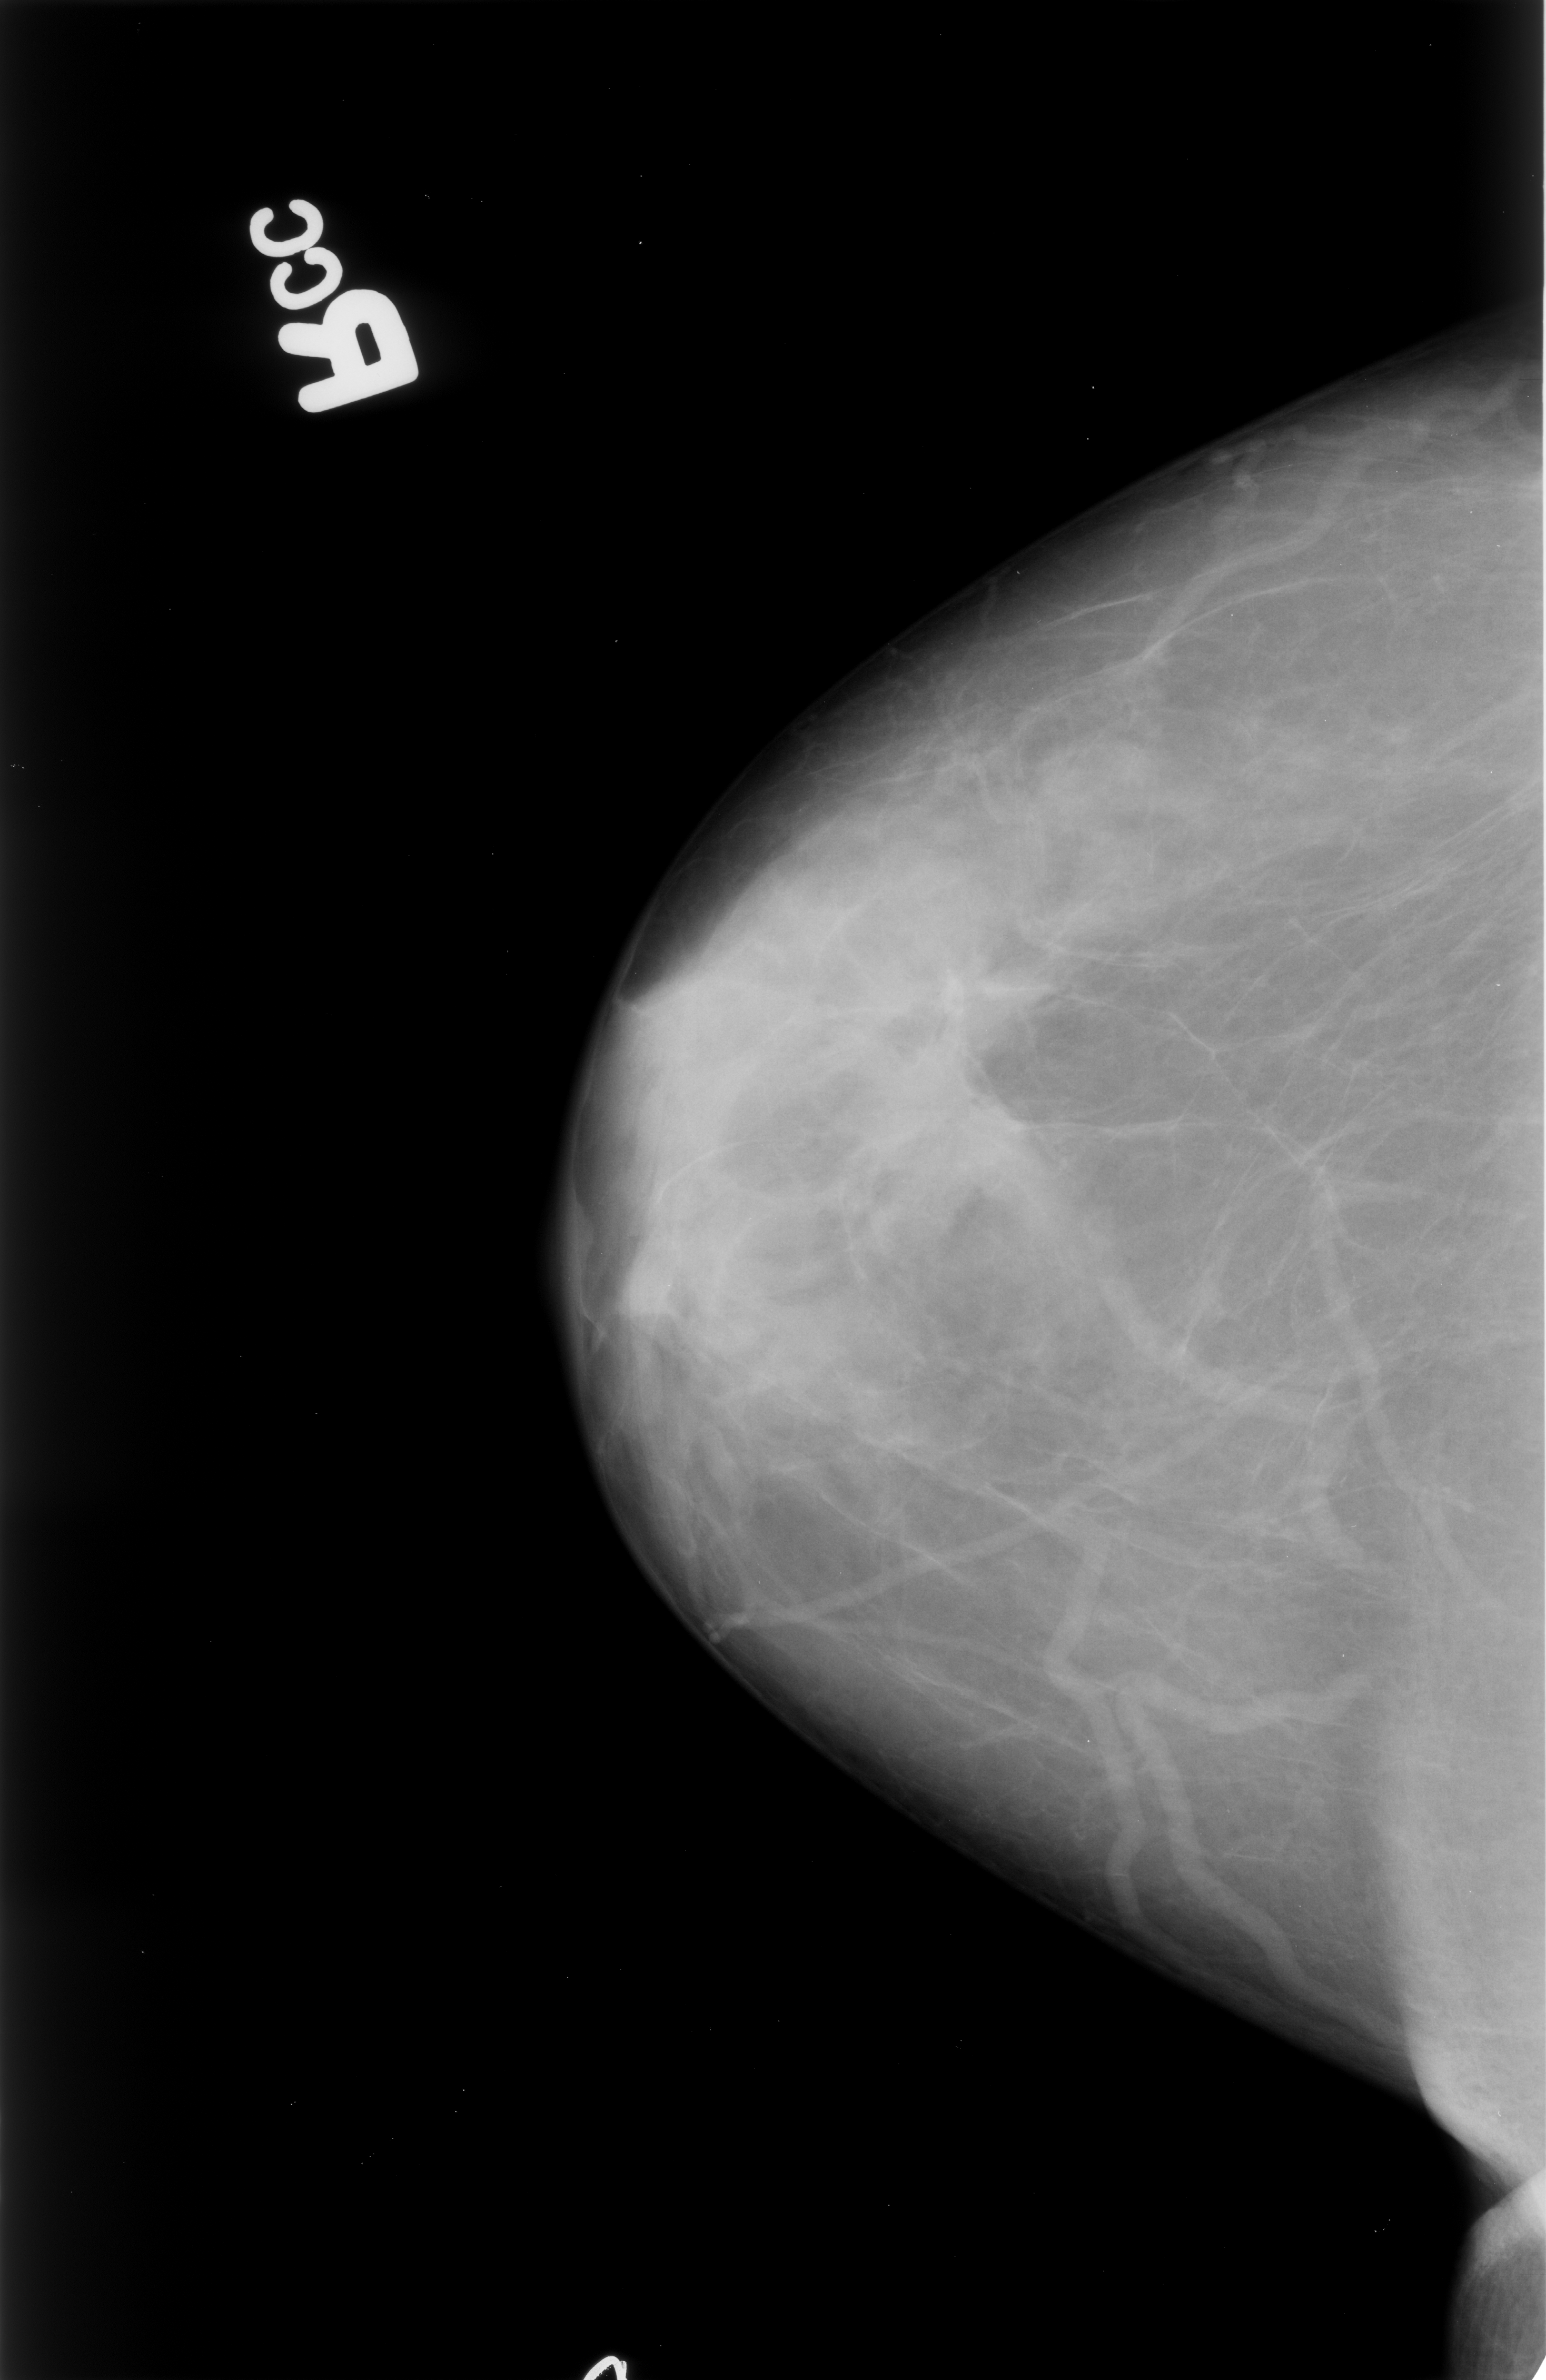
Digitized screen-film mammogram; right breast; craniocaudal (CC) view; 1546 × 2380 image matrix.
Expert-marked regions of interest on this film, with their recorded descriptors:
- mass, shape irregular / architectural distortion, margins spiculated; BI-RADS assessment category 4; subtlety rating 2 on a 1 (subtle) to 5 (obvious) scale; pathology (as recorded): malignant: bounding box <856,1047,1034,1210> (left, top, right, bottom; pixels)